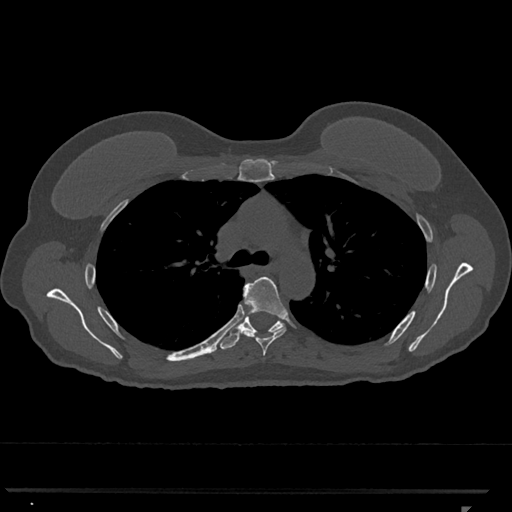
CT including the spine, one axial slice. Slice 789 of 793 in the series (ordered by position). Reconstruction kernel Br40s/3. 120 kVp. Bone window (W 1800 / L 400 HU). 0.5 mm slice thickness. 512 × 512 image matrix. Patient: female, 62 years. Case-level facts recorded for this patient, not image findings: primary cancer: renal.
Outlined on this slice (semi-automatic segmentation, software-assisted and operator-edited):
- T5 vertebra: bounding box [x1, y1, x2, y2] px = [240, 277, 288, 356]
- T6 vertebra: [220, 288, 283, 350]